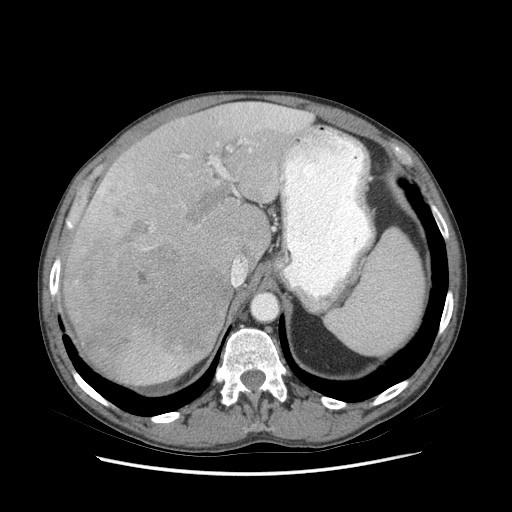
Contrast-enhanced abdominal CT (liver protocol), one axial slice. Position 56 of 89 along the scan axis. Reconstruction kernel STANDARD. 140 kVp. Soft-tissue window (W 400 / L 40 HU). 2.5 mm slice thickness. 512 × 512 image matrix, field of view 380 × 380 mm. From the clinical record (not read from this slice): diagnosis: hepatocellular carcinoma (patient treated with transarterial chemoembolisation; whether this scan precedes or follows treatment is not stated here); TNM stage (as recorded): Stage-IIIB; Child-Pugh class: A.
Annotated regions visible in this slice (semi-automatic segmentation, software-assisted and operator-edited):
- liver parenchyma outside the tumour (the mass and vessels are separate outlines, so this box may not span the whole liver): bounding box [x1, y1, x2, y2] px = [62, 102, 310, 384]
- mass: [65, 217, 228, 378]
- liver vessels: [91, 103, 308, 266]